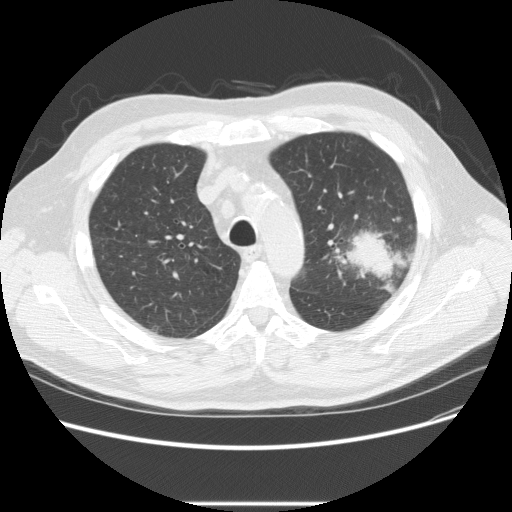
Low-dose screening chest CT, one axial slice. Slice 170 of 233 in the series (ordered by position). 120 kVp. Lung window (W 1500 / L -600 HU). 512 × 512 image matrix, field of view 380 × 380 mm.
Annotated regions visible in this slice (outlined manually by an expert reader):
- lesion 1 (tumor, upper lobe of left lung): bounding box [x1, y1, x2, y2] px = [346, 227, 399, 281]